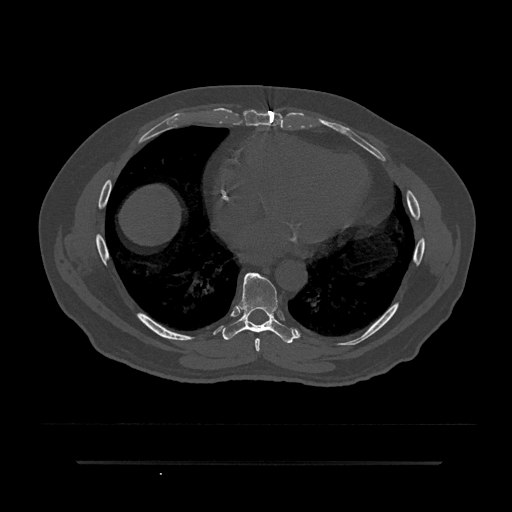
CT including the spine, one axial slice; reconstruction kernel Br40s/3; bone window (W 1800 / L 400 HU); 0.5 mm slice thickness; 512 × 512 image matrix, field of view 464 × 464 mm. Patient: male, 59 years. From the clinical record (not read from this slice): primary cancer: bile ducts; vertebrae with lytic lesions (as recorded): T10.
Outlined on this slice (semi-automatic segmentation, software-assisted and operator-edited):
- T7 vertebra: bounding box (x1, y1, x2, y2) in pixels: (255, 338, 260, 352)
- T8 vertebra: (222, 272, 296, 343)